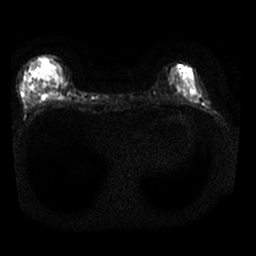
Breast MRI, one axial slice. Position 8 of 25 along the scan axis. Diffusion-weighted series; image 2 of 4 stored at this slice position (different b-values; order by instance number). 1.5 T. 4 mm slice thickness. 256 × 256 image matrix. Female patient.
Annotated regions visible in this slice (manually delineated by an expert):
- tumour on diffusion-weighted imaging: box from (x=52, y=70) to (x=59, y=78) px